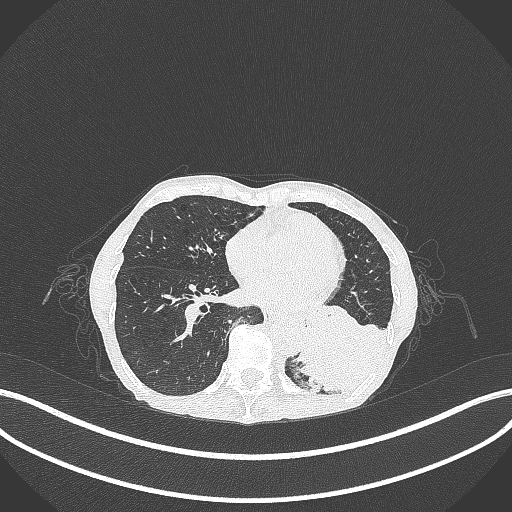
Chest CT, one axial slice. Position 97 of 347 along the scan axis. Reconstruction kernel B70f. 120 kVp. Lung window (W 1500 / L -600 HU). 1 mm slice thickness. 512 × 512 image matrix, field of view 400 × 400 mm. Patient: female, 70 years. Case-level facts recorded for this patient, not image findings: clinical TNM (as recorded): T3 N0 M0; histopathological grade: G3.
Annotated regions visible in this slice (bounding box drawn by a radiologist):
- lung tumour (recorded histology: small cell carcinoma): bounding box <297,317,401,407> (left, top, right, bottom; pixels)